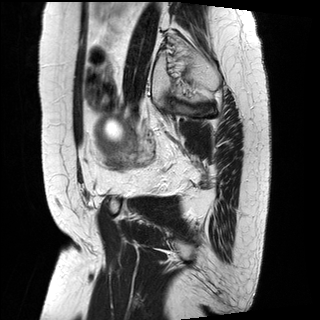
Pelvic MRI for cervical cancer, one sagittal slice. Position 25 of 29 along the scan axis. T2-weighted. 1.5 T. TE 89 ms, TR 2930 ms. 4 mm slice thickness. 320 × 320 image matrix, field of view 260 × 260 mm. Patient: female, 49 years.
Annotated regions visible in this slice (expert manual segmentation):
- uterus and cervix: box from (x=94, y=112) to (x=132, y=156) px